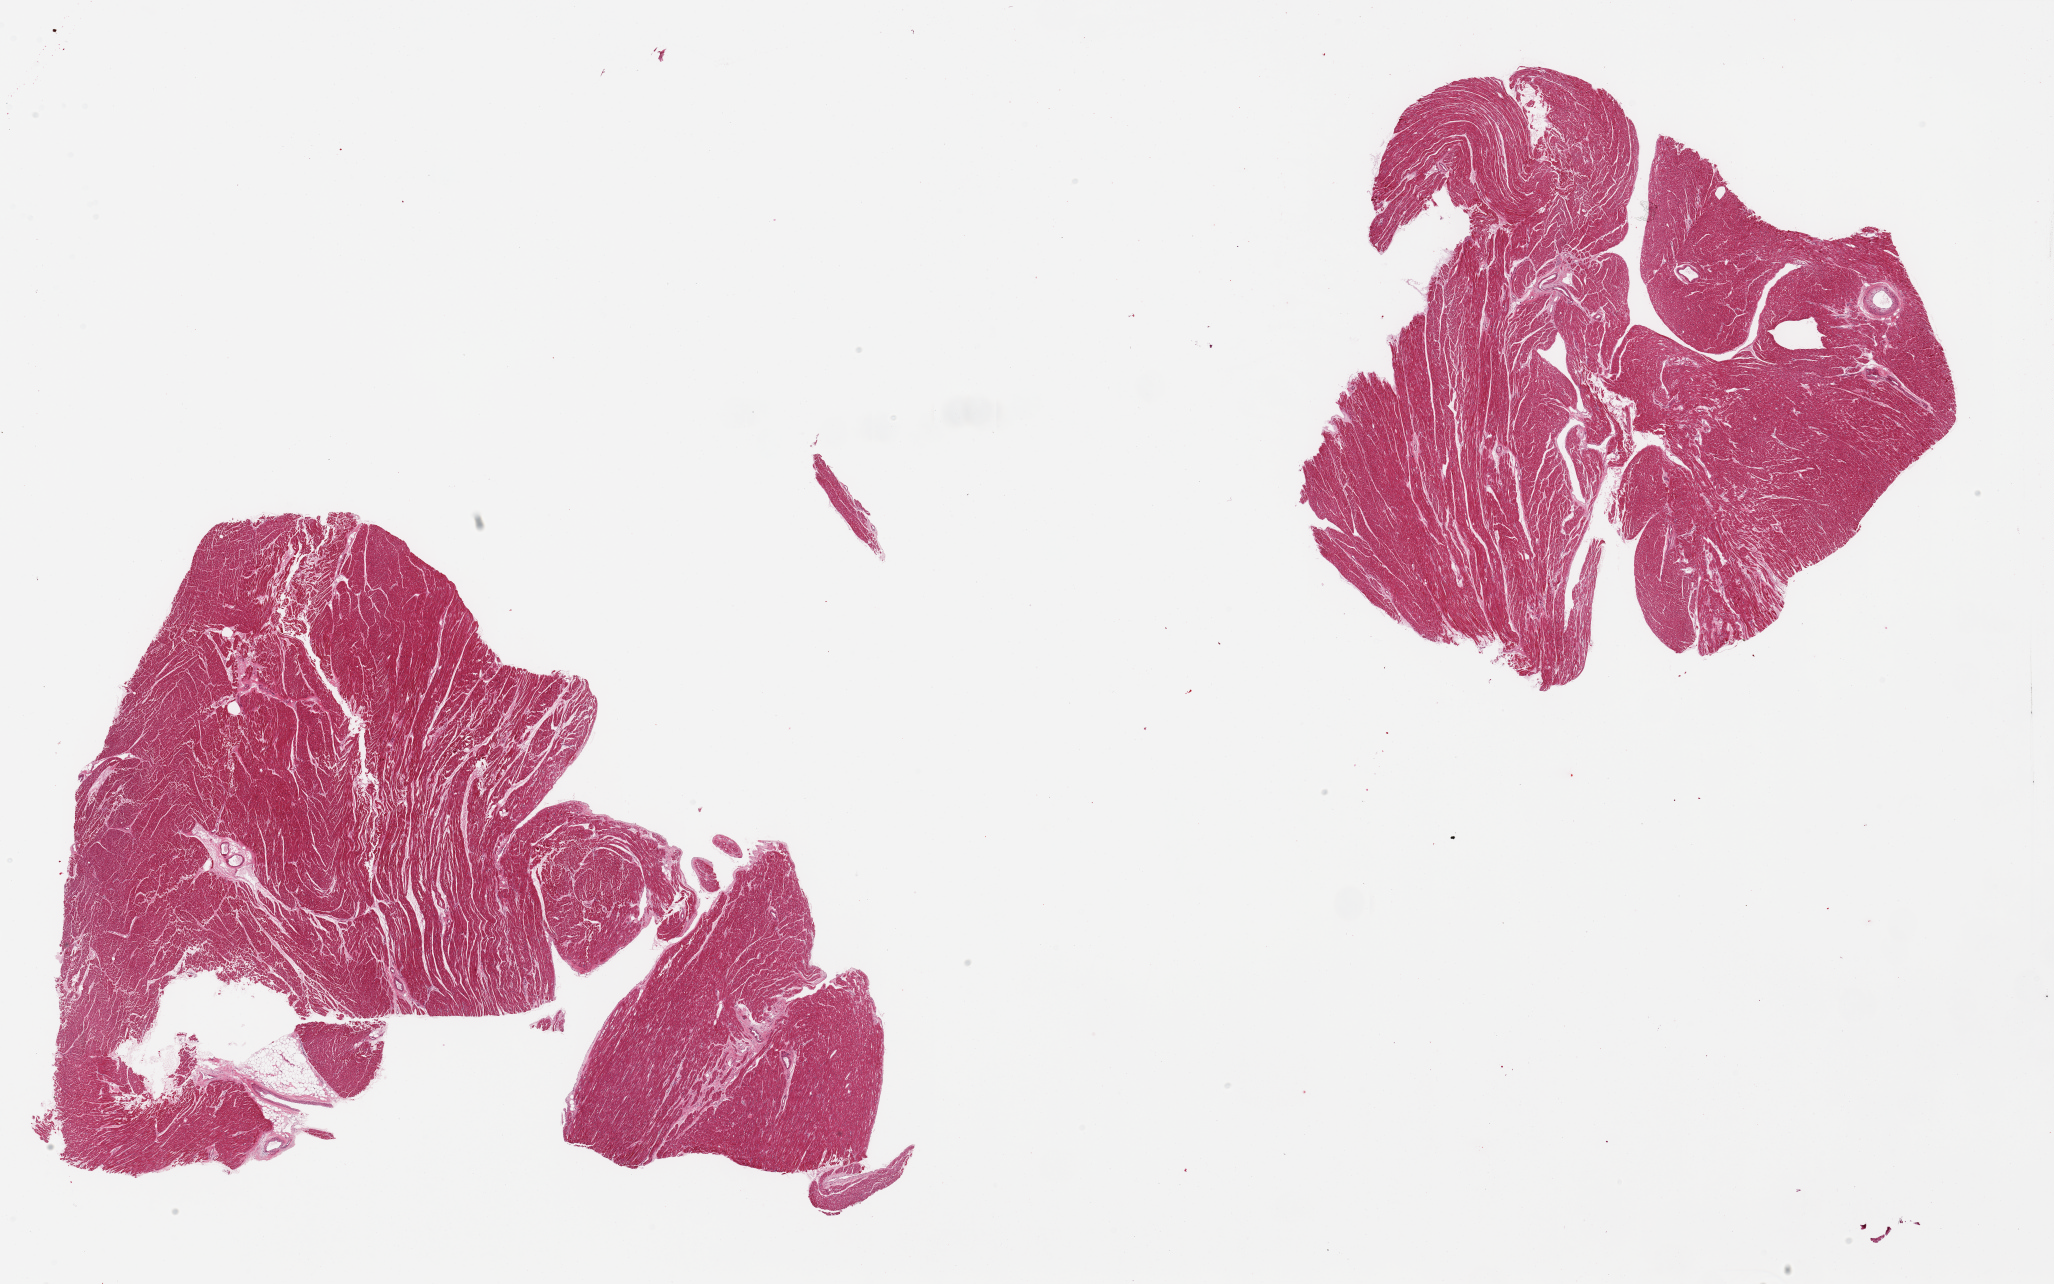
Digitized hematoxylin and eosin (H&E)-stained section, a low-resolution overview of the entire scanned area, about 32.5 x 20.3 mm (from a 20x scan); PAXgene-fixed paraffin-embedded (PFPE) section; target tissue: heart; donor tissue sample.
Pathologist's review note for this sample: 2 pieces.